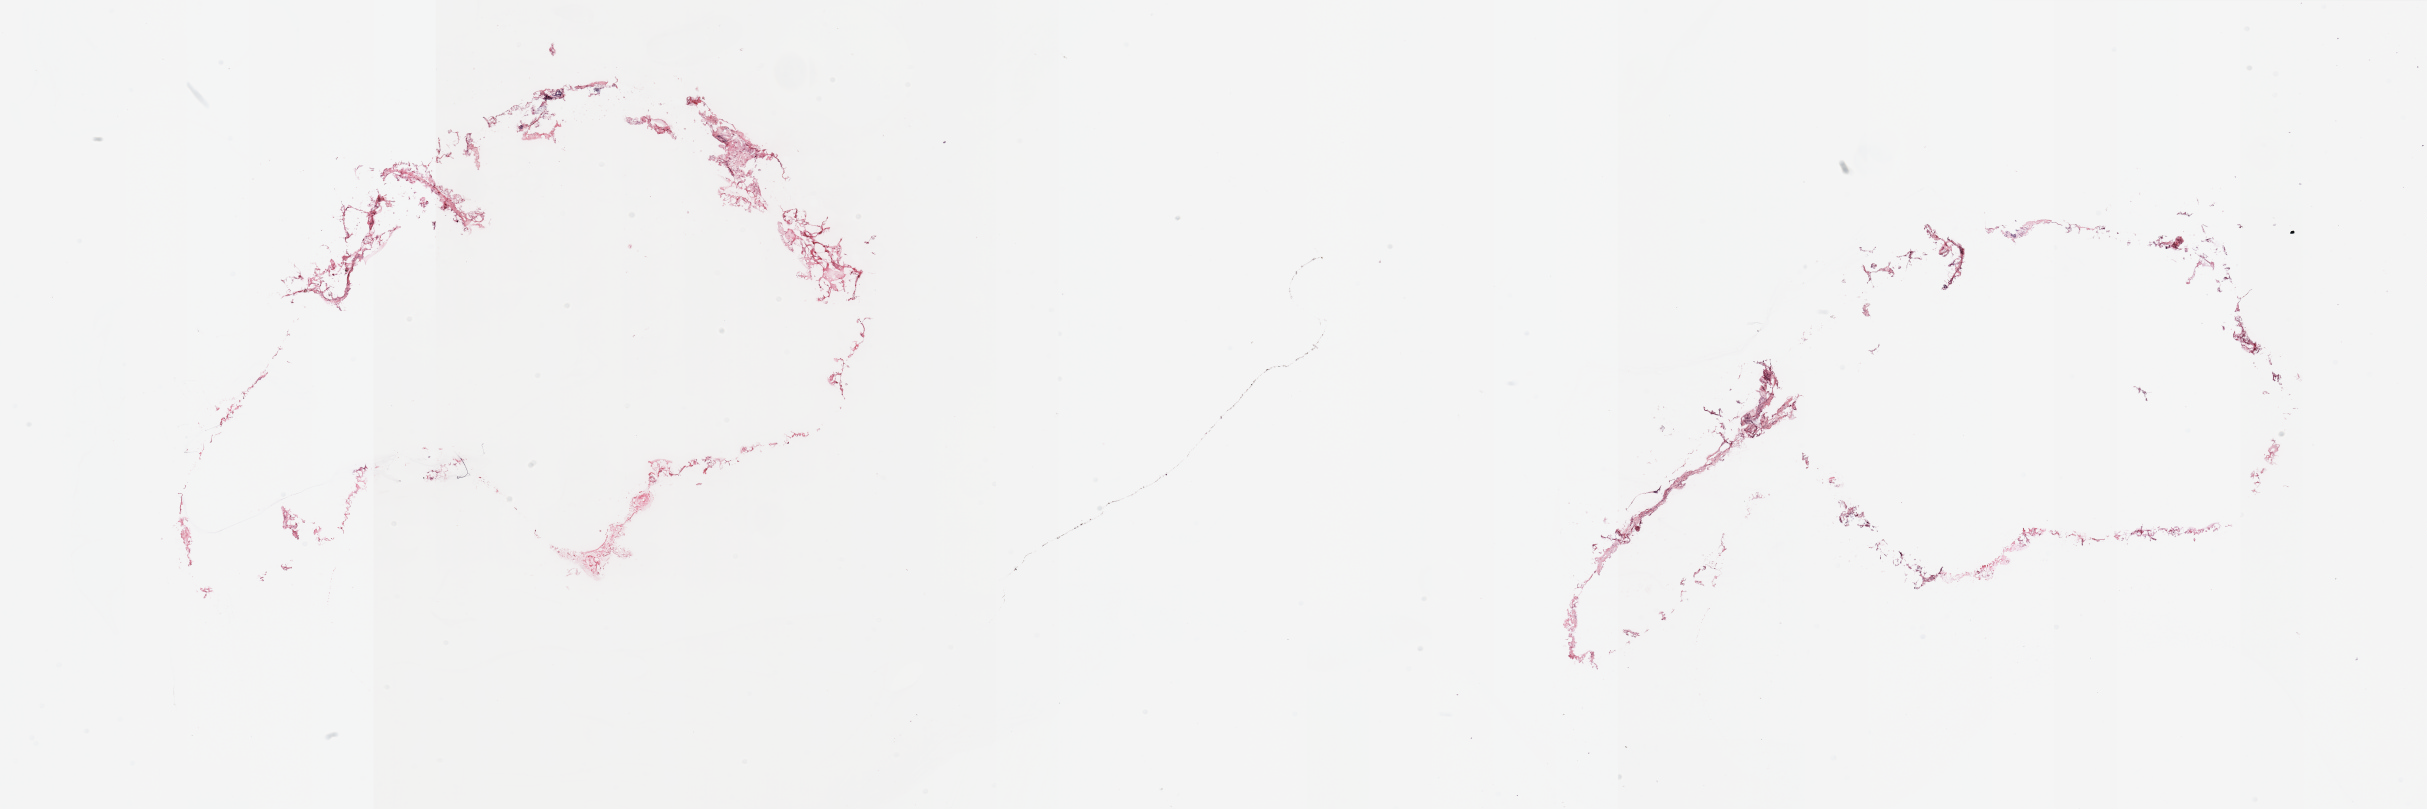
Digitized Hematoxylin and eosin (H&E) stained tissue section (whole slide) — low-resolution overview of the scanned area, about 38.4 x 12.8 mm (slide scanned at 20x), breast, tissue type not recorded.
Patient diagnosis (cohort enrolment): breast cancer (breast).